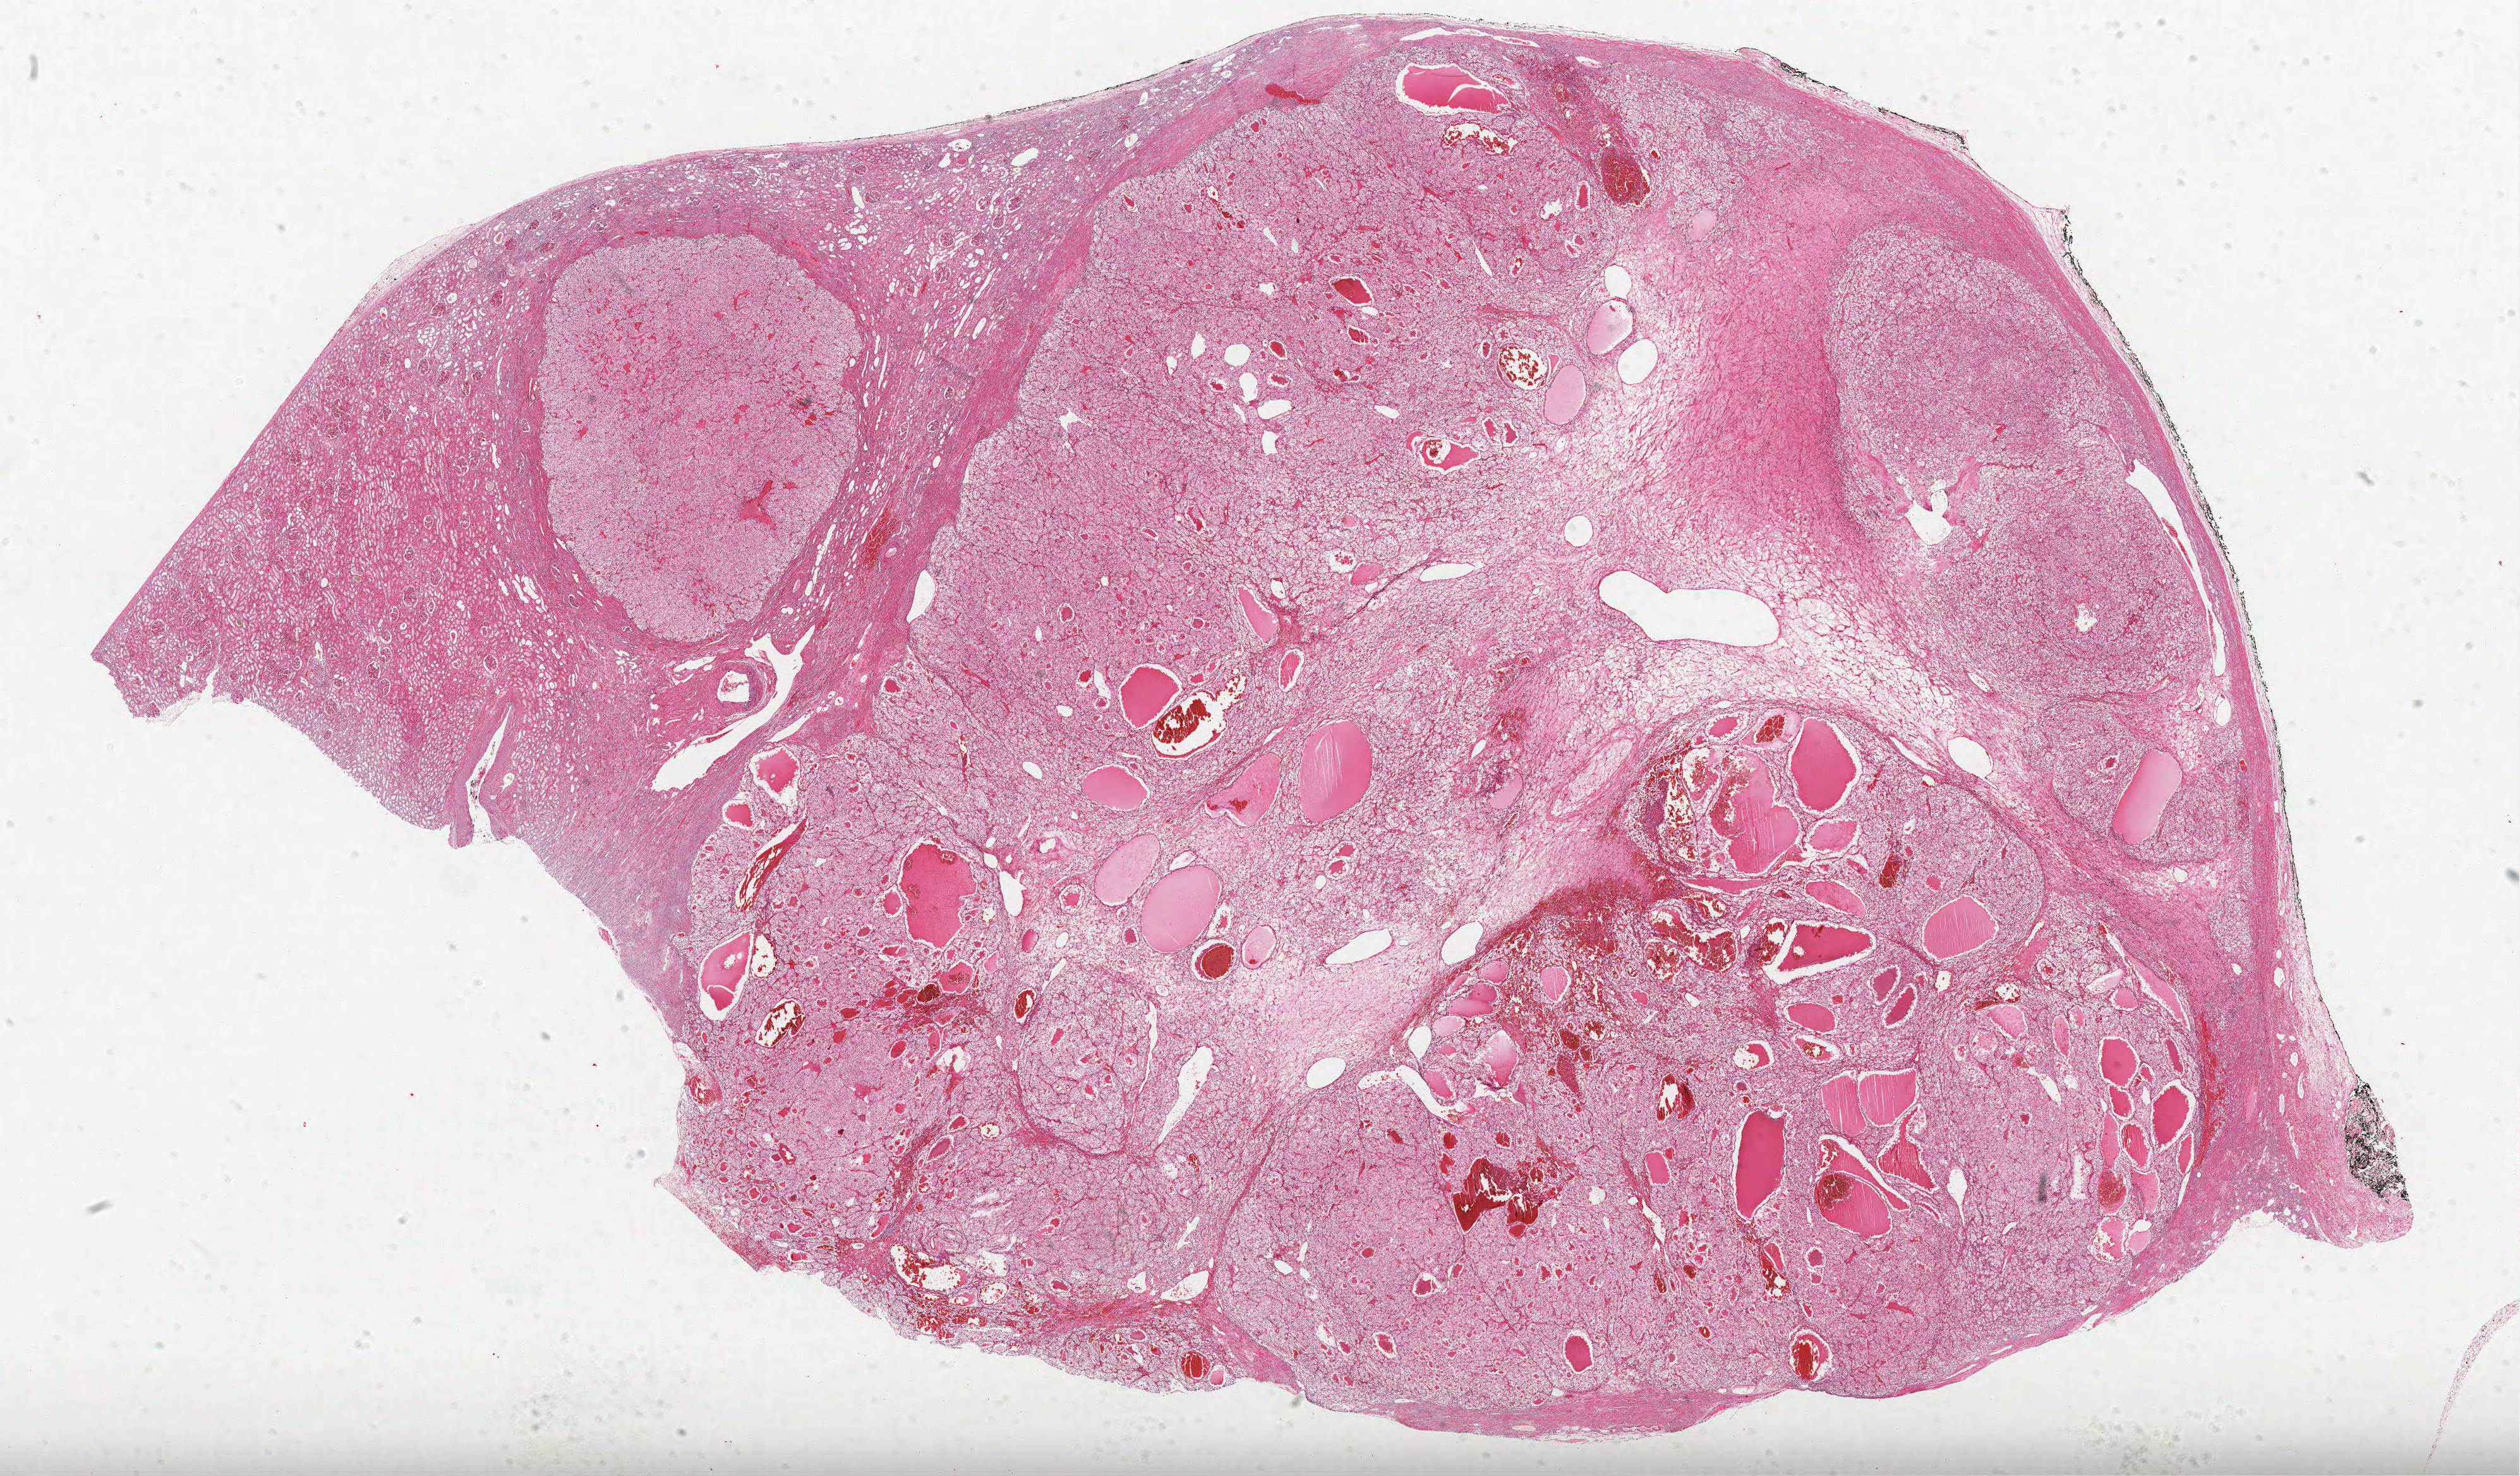
H&E-stained whole-slide image — a low-resolution overview of the entire scanned area, about 31.9 x 18.7 mm (slide scanned at 40x); FFPE section; primary tumour sample from the kidney. Patient: female, age at initial diagnosis 51 years. Histologic grade: G2 (moderately differentiated).
* TNM: T3a NX M0
* laterality: left
* AJCC pathologic stage: III
* histologic diagnosis: Clear cell adenocarcinoma, NOS